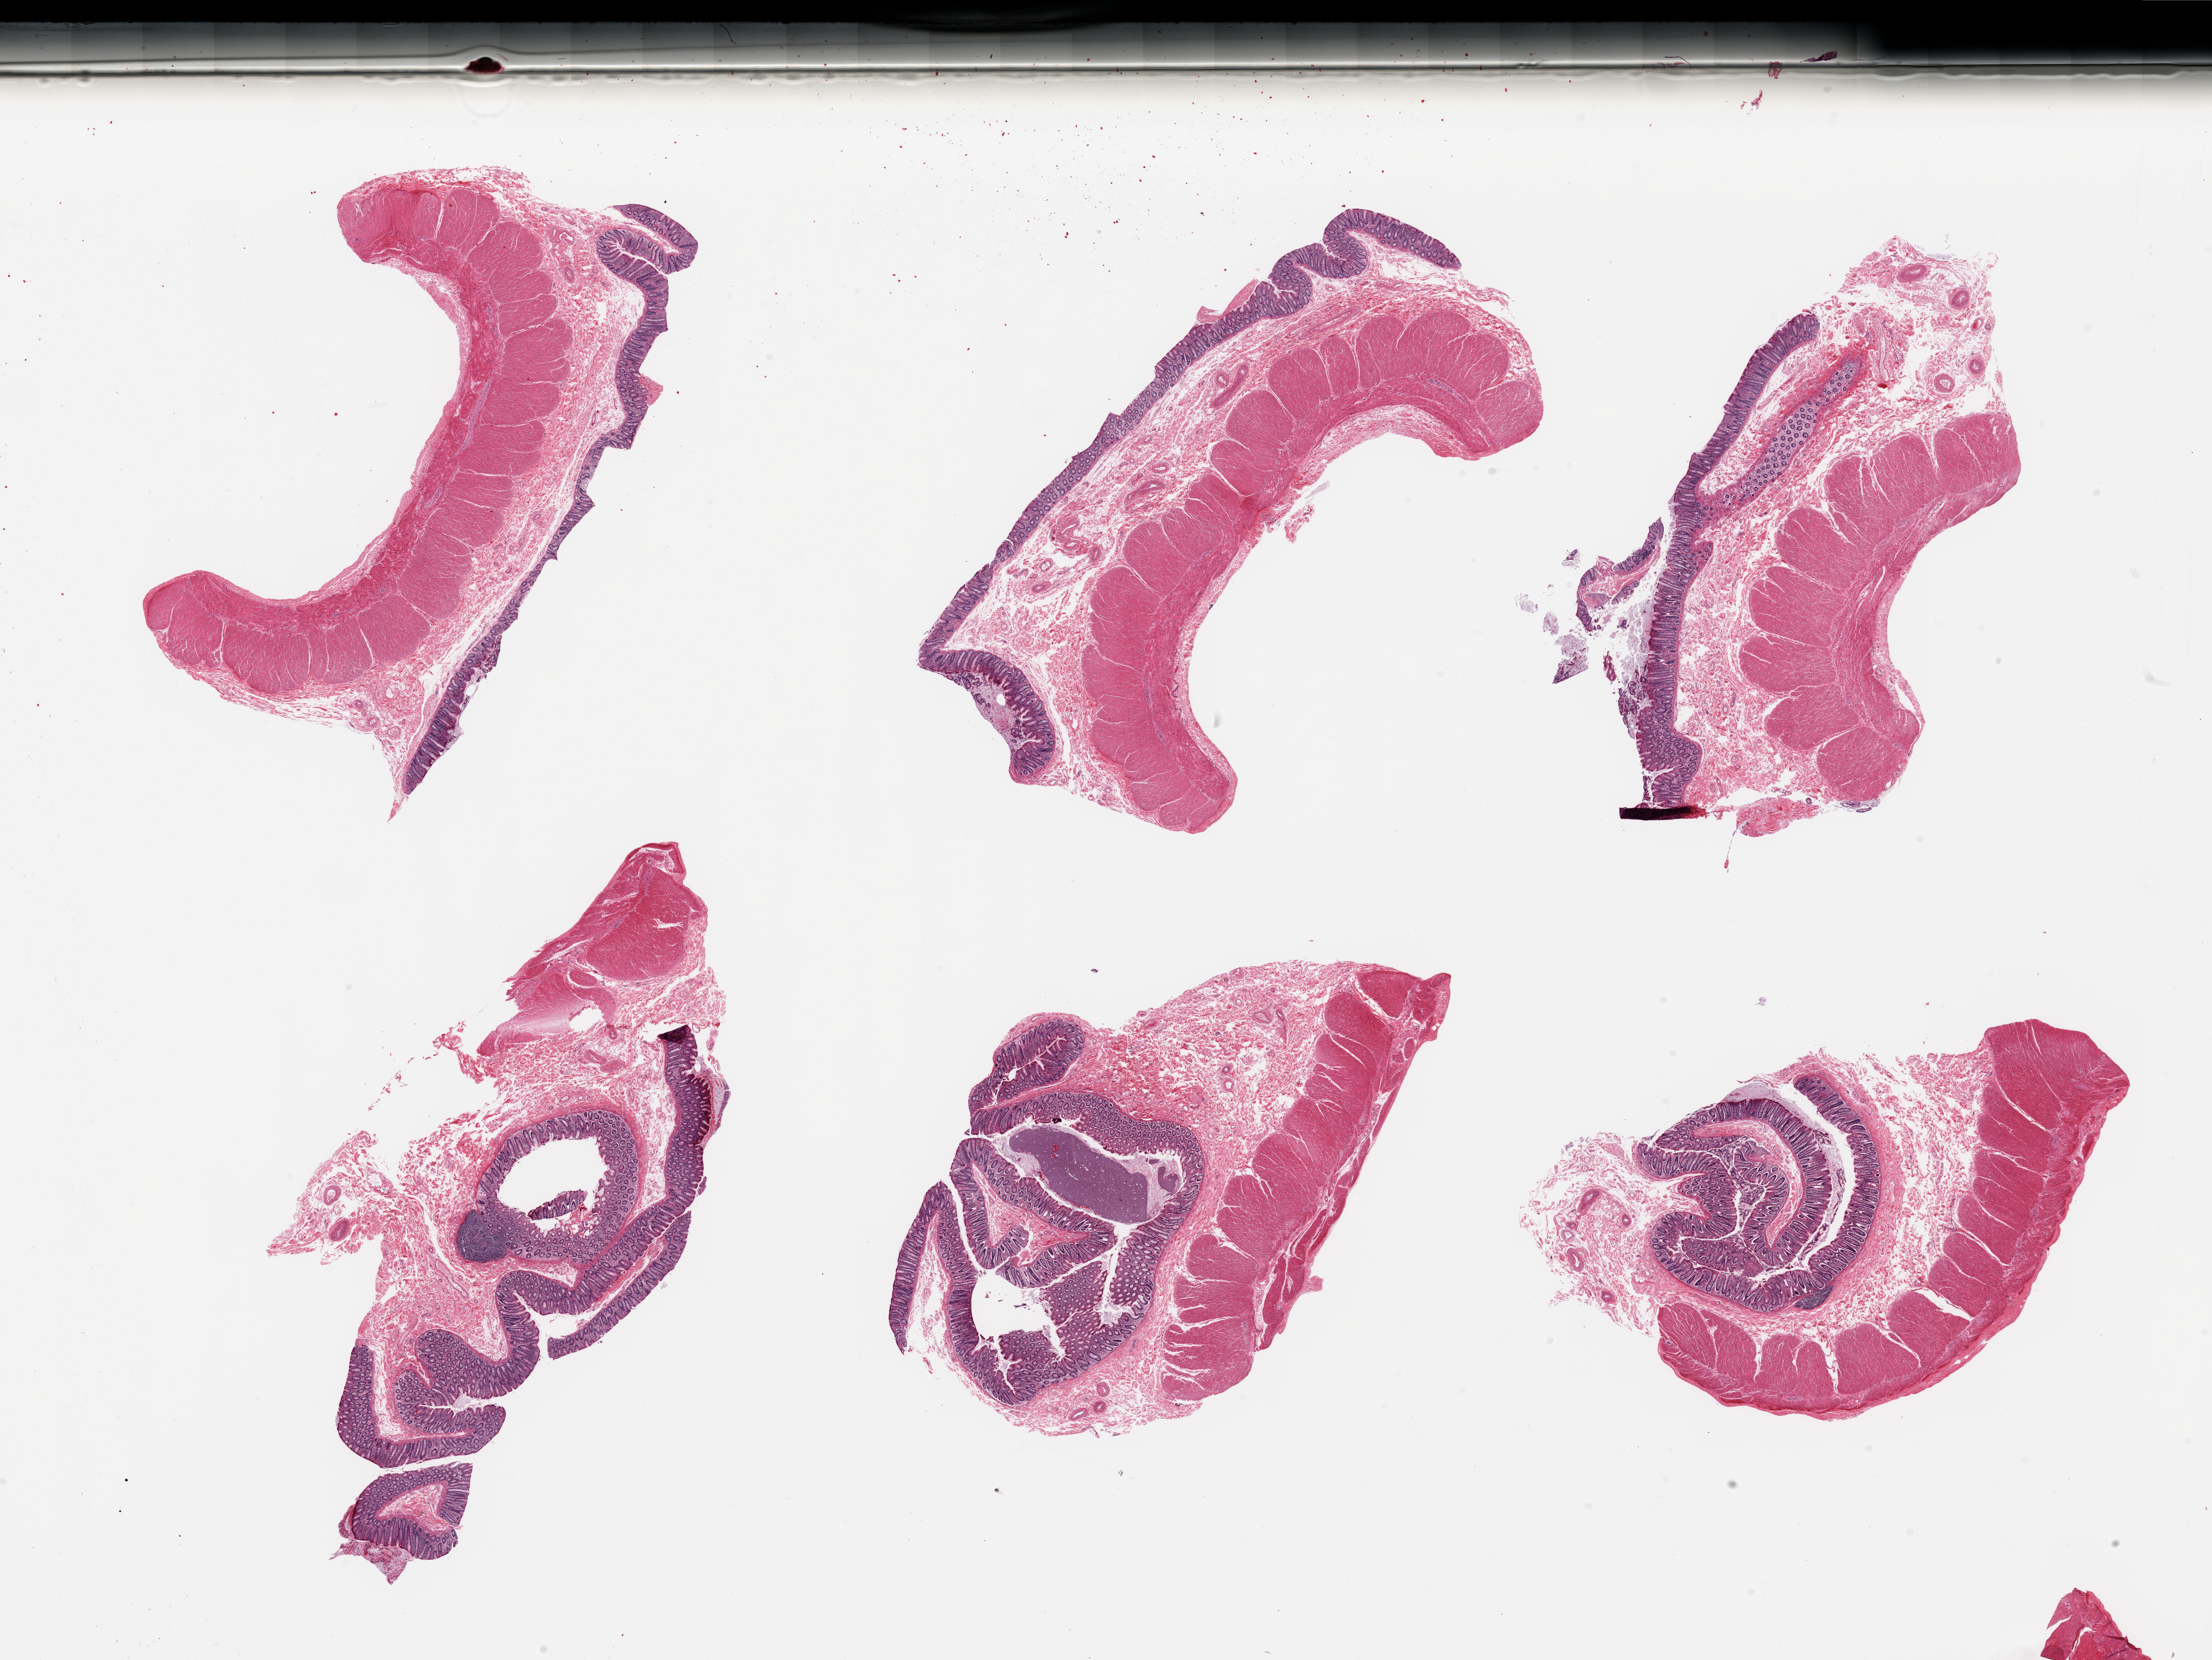
Whole-slide image, H&E stain, a low-resolution overview of the entire scanned area, about 30.5 x 22.9 mm, PAXgene-fixed paraffin-embedded (PFPE) section, target tissue: transverse colon, tissue donor sample. Donor: male.
Review note (as recorded): 6 pieces, target mucosa well-preserved, ~10-20% of thickness.